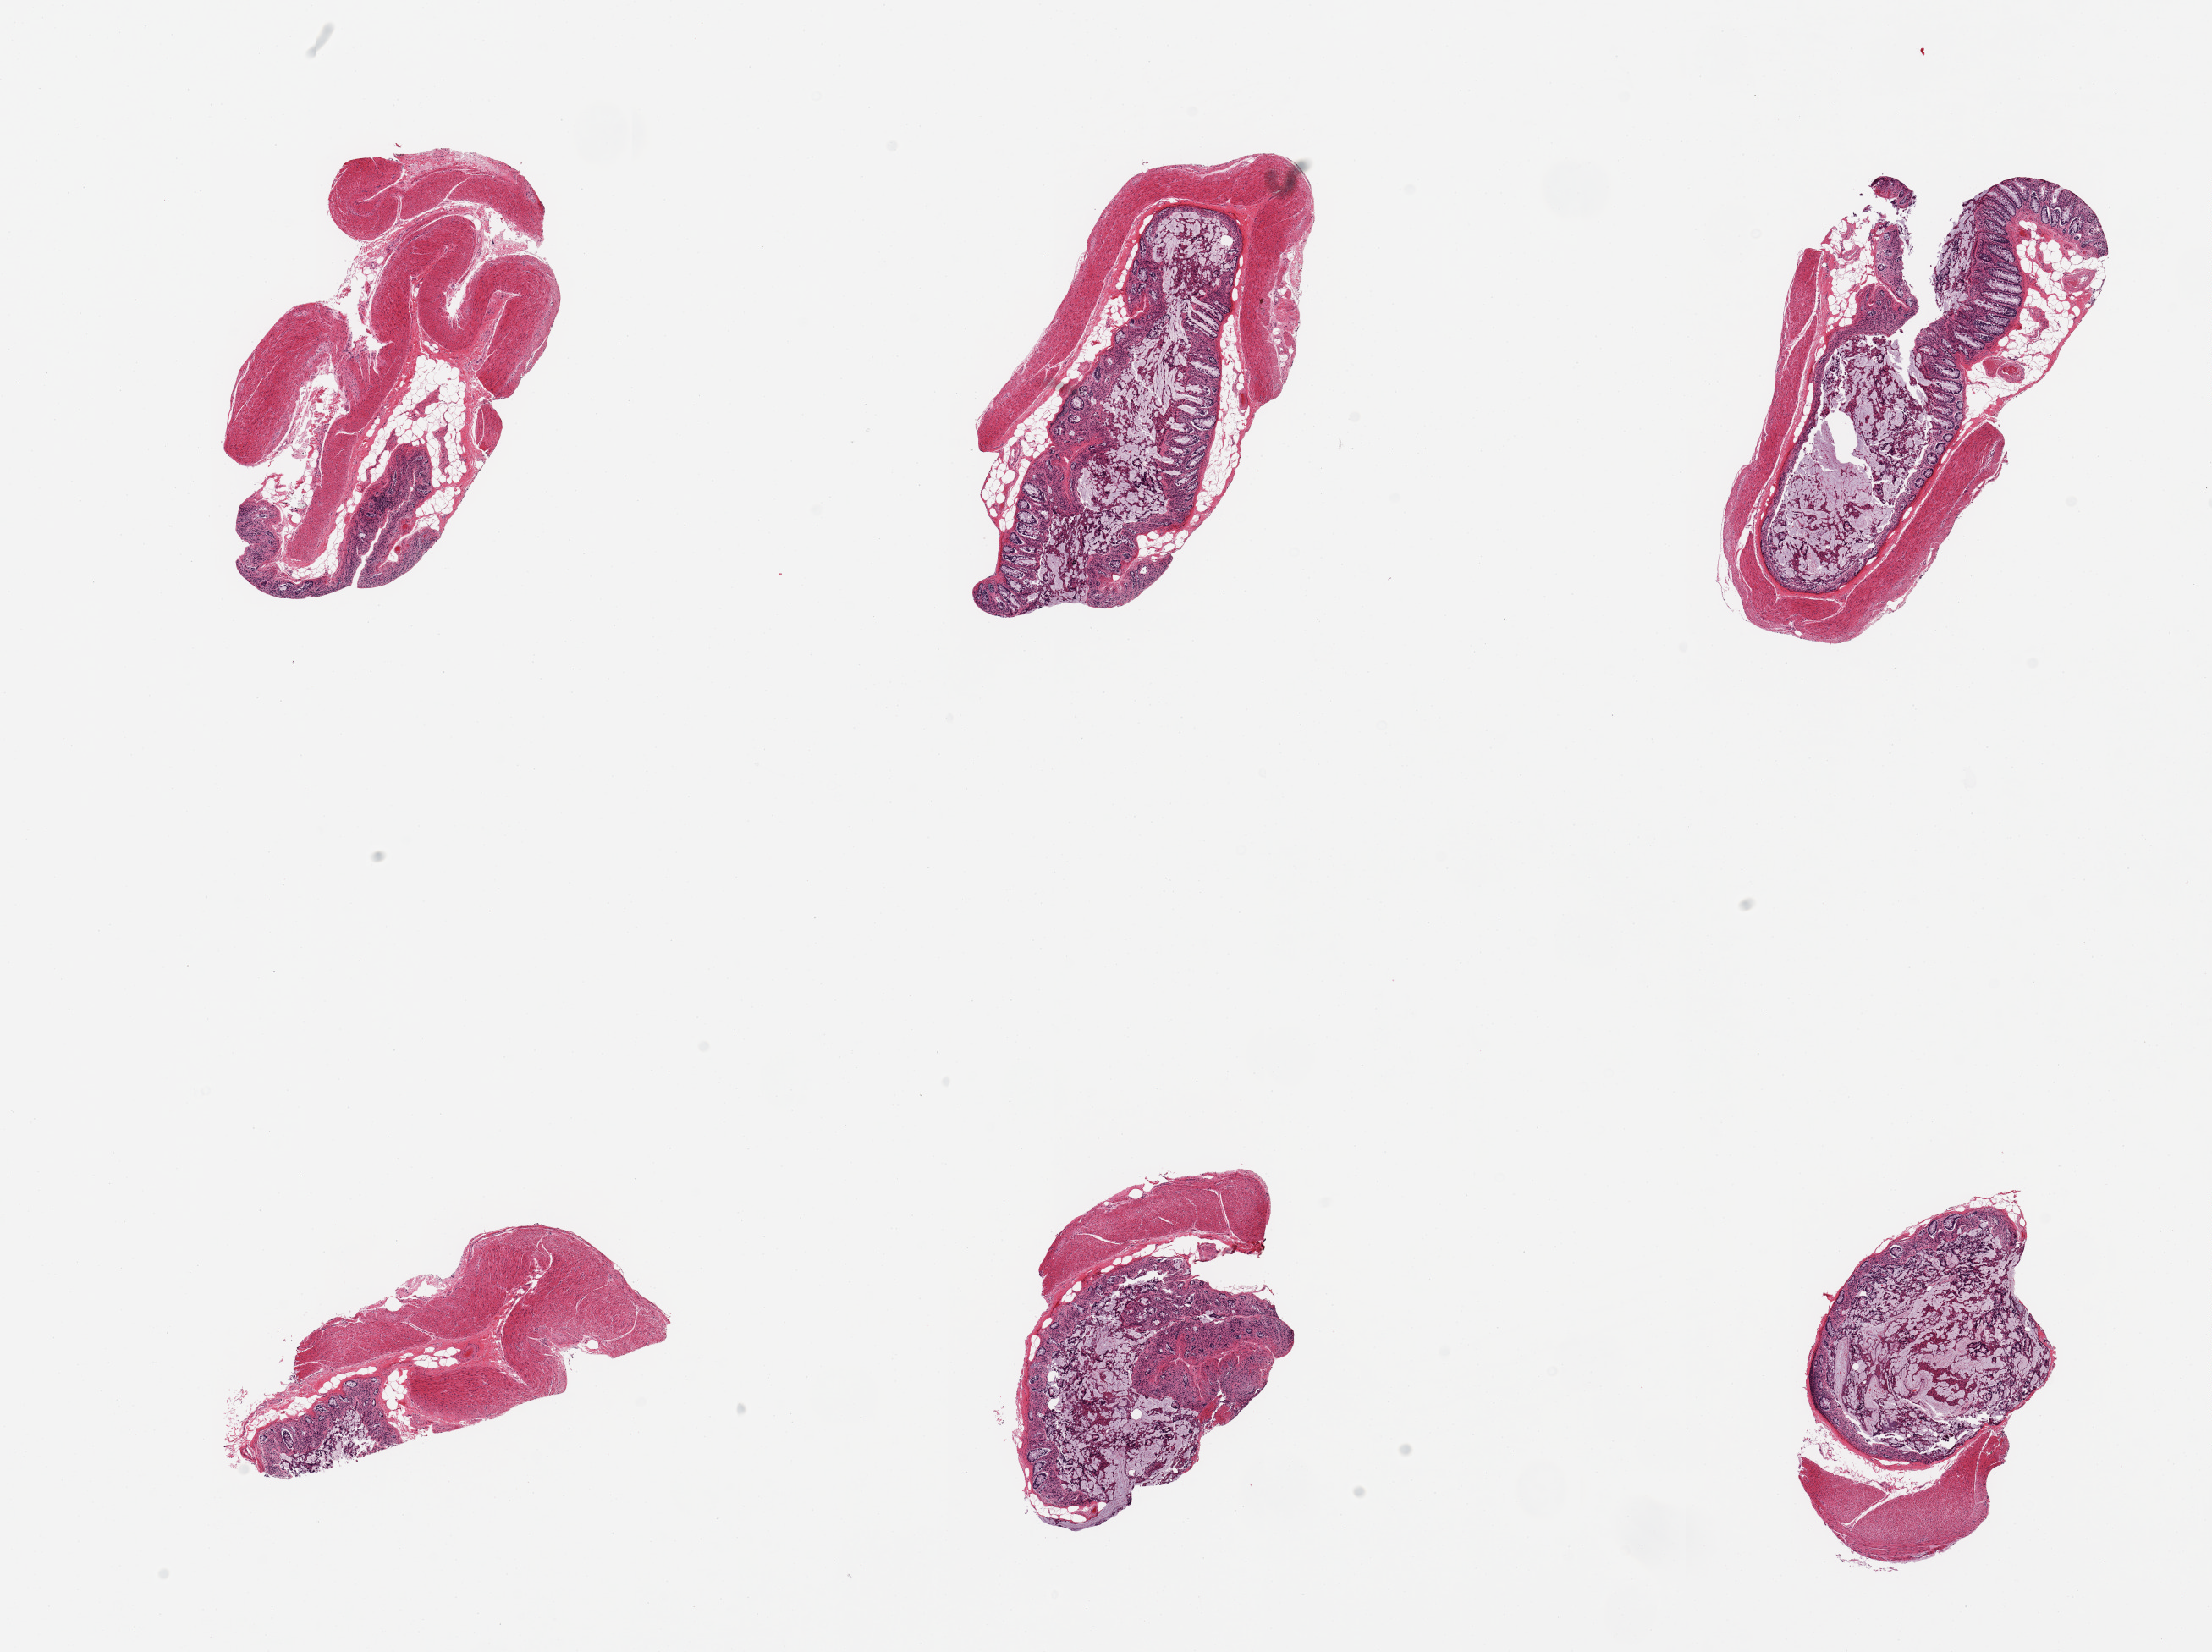
Whole-slide image, haematoxylin and eosin stain — a low-resolution overview of the entire scanned area, about 20.7 x 15.4 mm. PAXgene-fixed, paraffin-embedded tissue. Sampled site (target tissue): transverse colon. Donor tissue sample. Male donor.
Pathologist's review note for this sample: 6 pieces; lots of extruded mucus in 4 of 6 pieces.